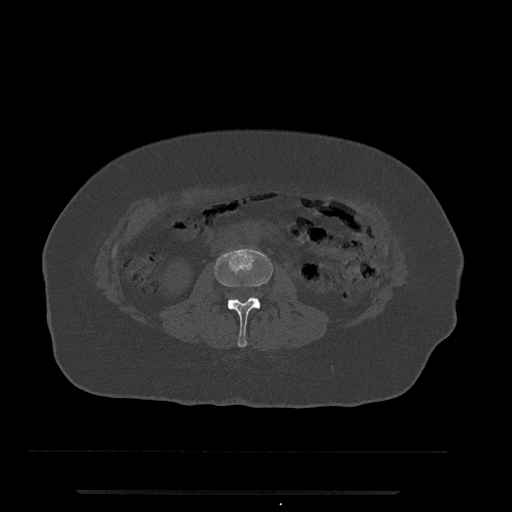
CT including the spine, one axial slice. Slice 19 of 797 in the series (ordered by position). Reconstruction kernel Br40s/3. 120 kVp. Bone window (W 1800 / L 400 HU). 0.5 mm slice thickness. 512 × 512 image matrix. Female patient, age 51 years. From the clinical record (not read from this slice): primary cancer: neuro.
Annotated regions visible in this slice (semi-automatically segmented with operator editing):
- L2 vertebra: bounding box (x1, y1, x2, y2) in pixels: (214, 248, 273, 347)